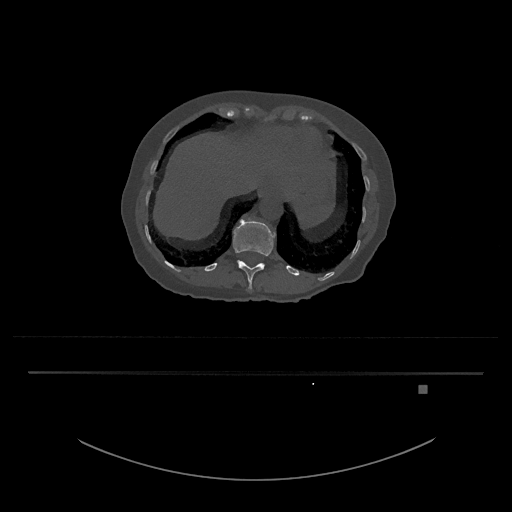
CT including the spine, one axial slice; reconstruction kernel Br40s/3; bone window (W 1800 / L 400 HU); 512 × 512 image matrix, field of view 500 × 500 mm. Patient: female, 57 years. From the clinical record (not read from this slice): primary cancer: cervical.
Structures marked on this image (semi-automatic segmentation, software-assisted and operator-edited):
- T12 vertebra: box from (x=233, y=219) to (x=276, y=290) px